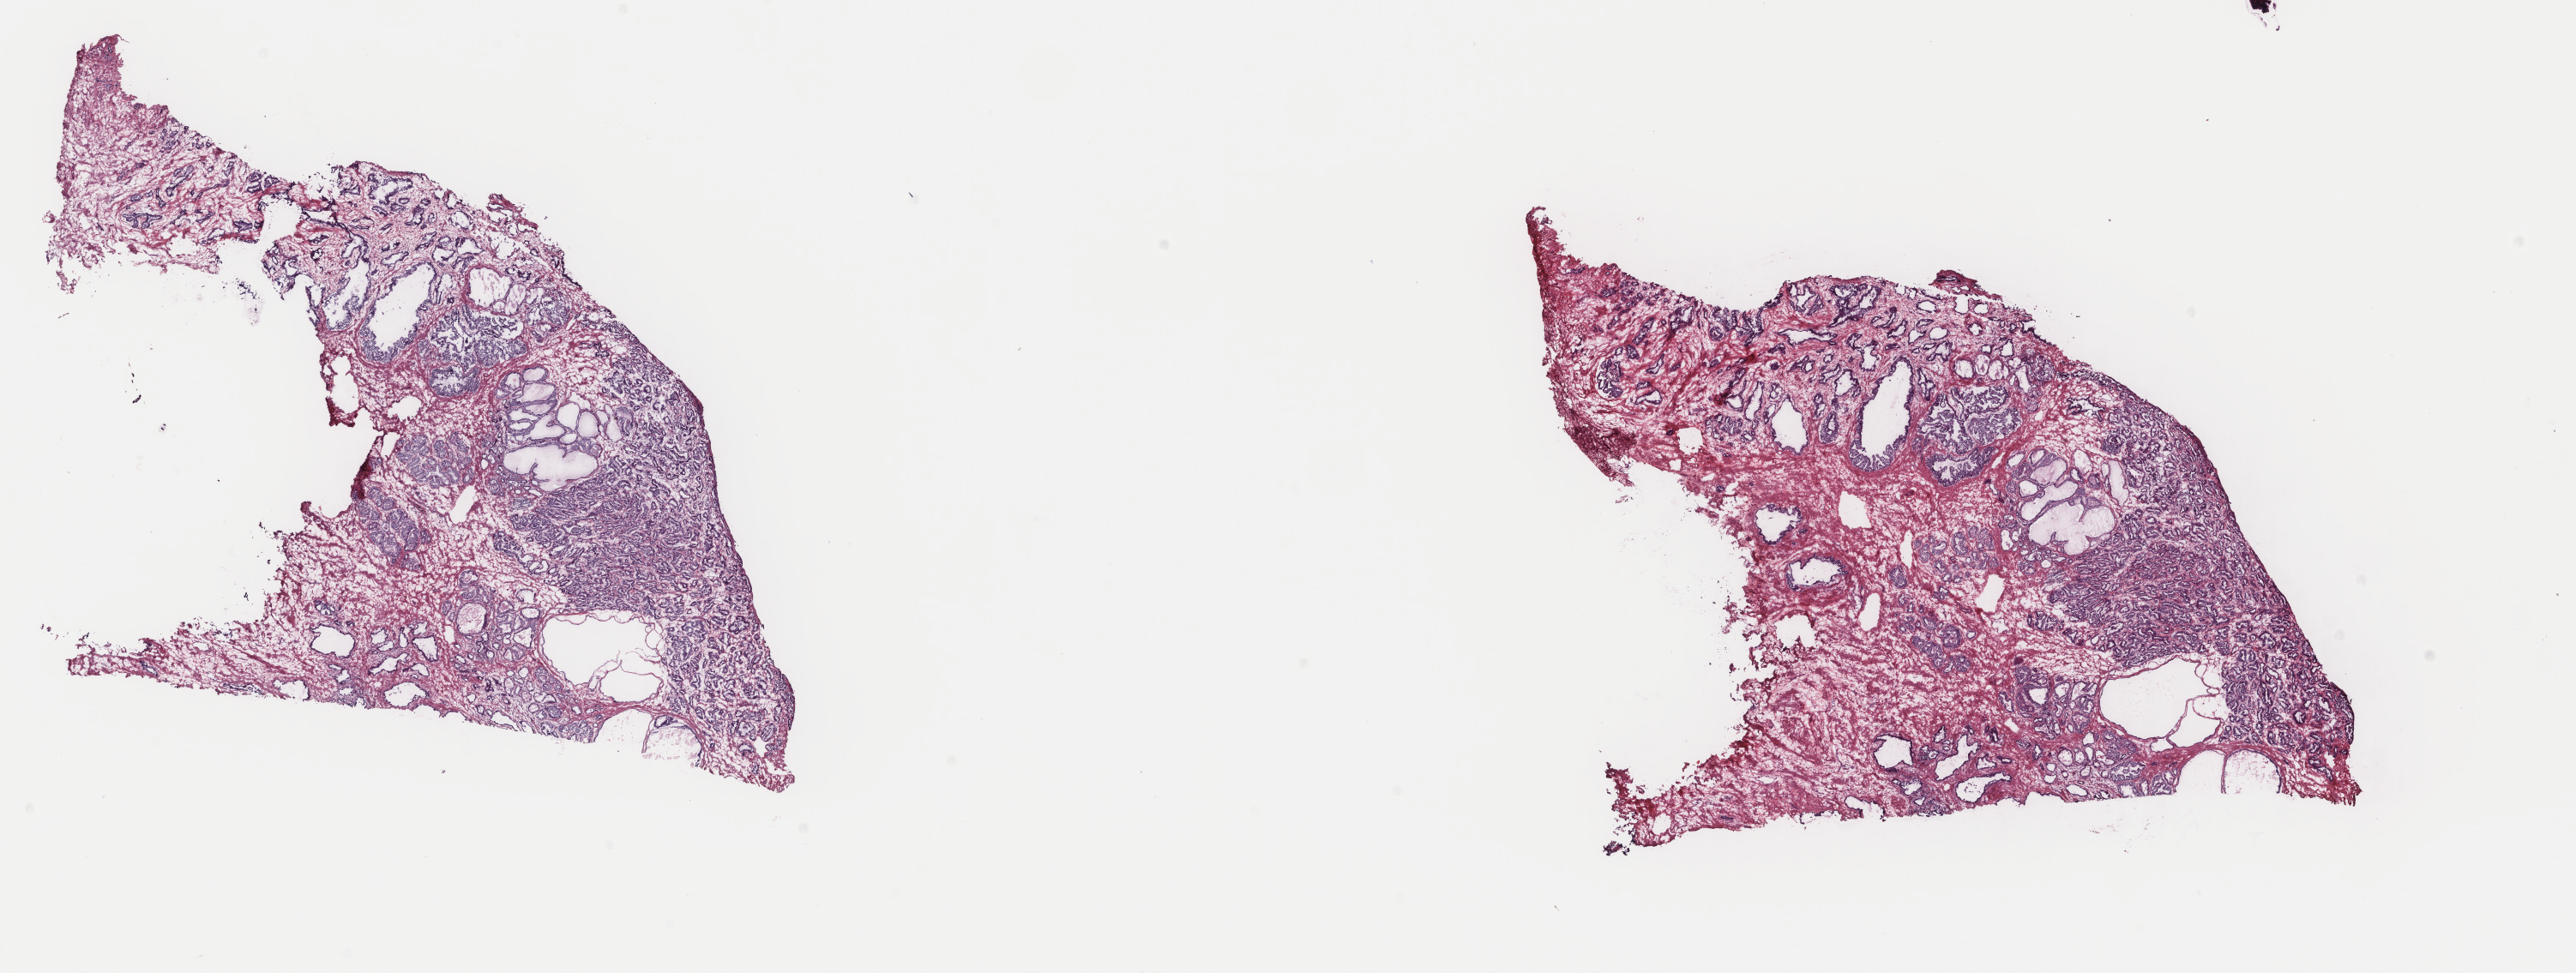
Hematoxylin and eosin (H&E) stained whole-slide image — shown as a low-resolution overview of the whole scanned area (about 23.8 x 9.0 mm, slide scanned at 40x), frozen section from the top of the tissue portion, prostate, primary tumour sample. Male, age 57 years at initial diagnosis. Gleason score: 7 (3+4). Composition of this section per pathologist review: tumour cells 50%, tumour nuclei 60%, normal cells 20%, stromal cells 30%, necrosis 0%. Inflammatory infiltration, as recorded: lymphocyte infiltration 0%, monocyte infiltration 0%, neutrophil infiltration 0%.
Laterality: bilateral. Diagnosis: Adenocarcinoma, NOS (prostate gland).